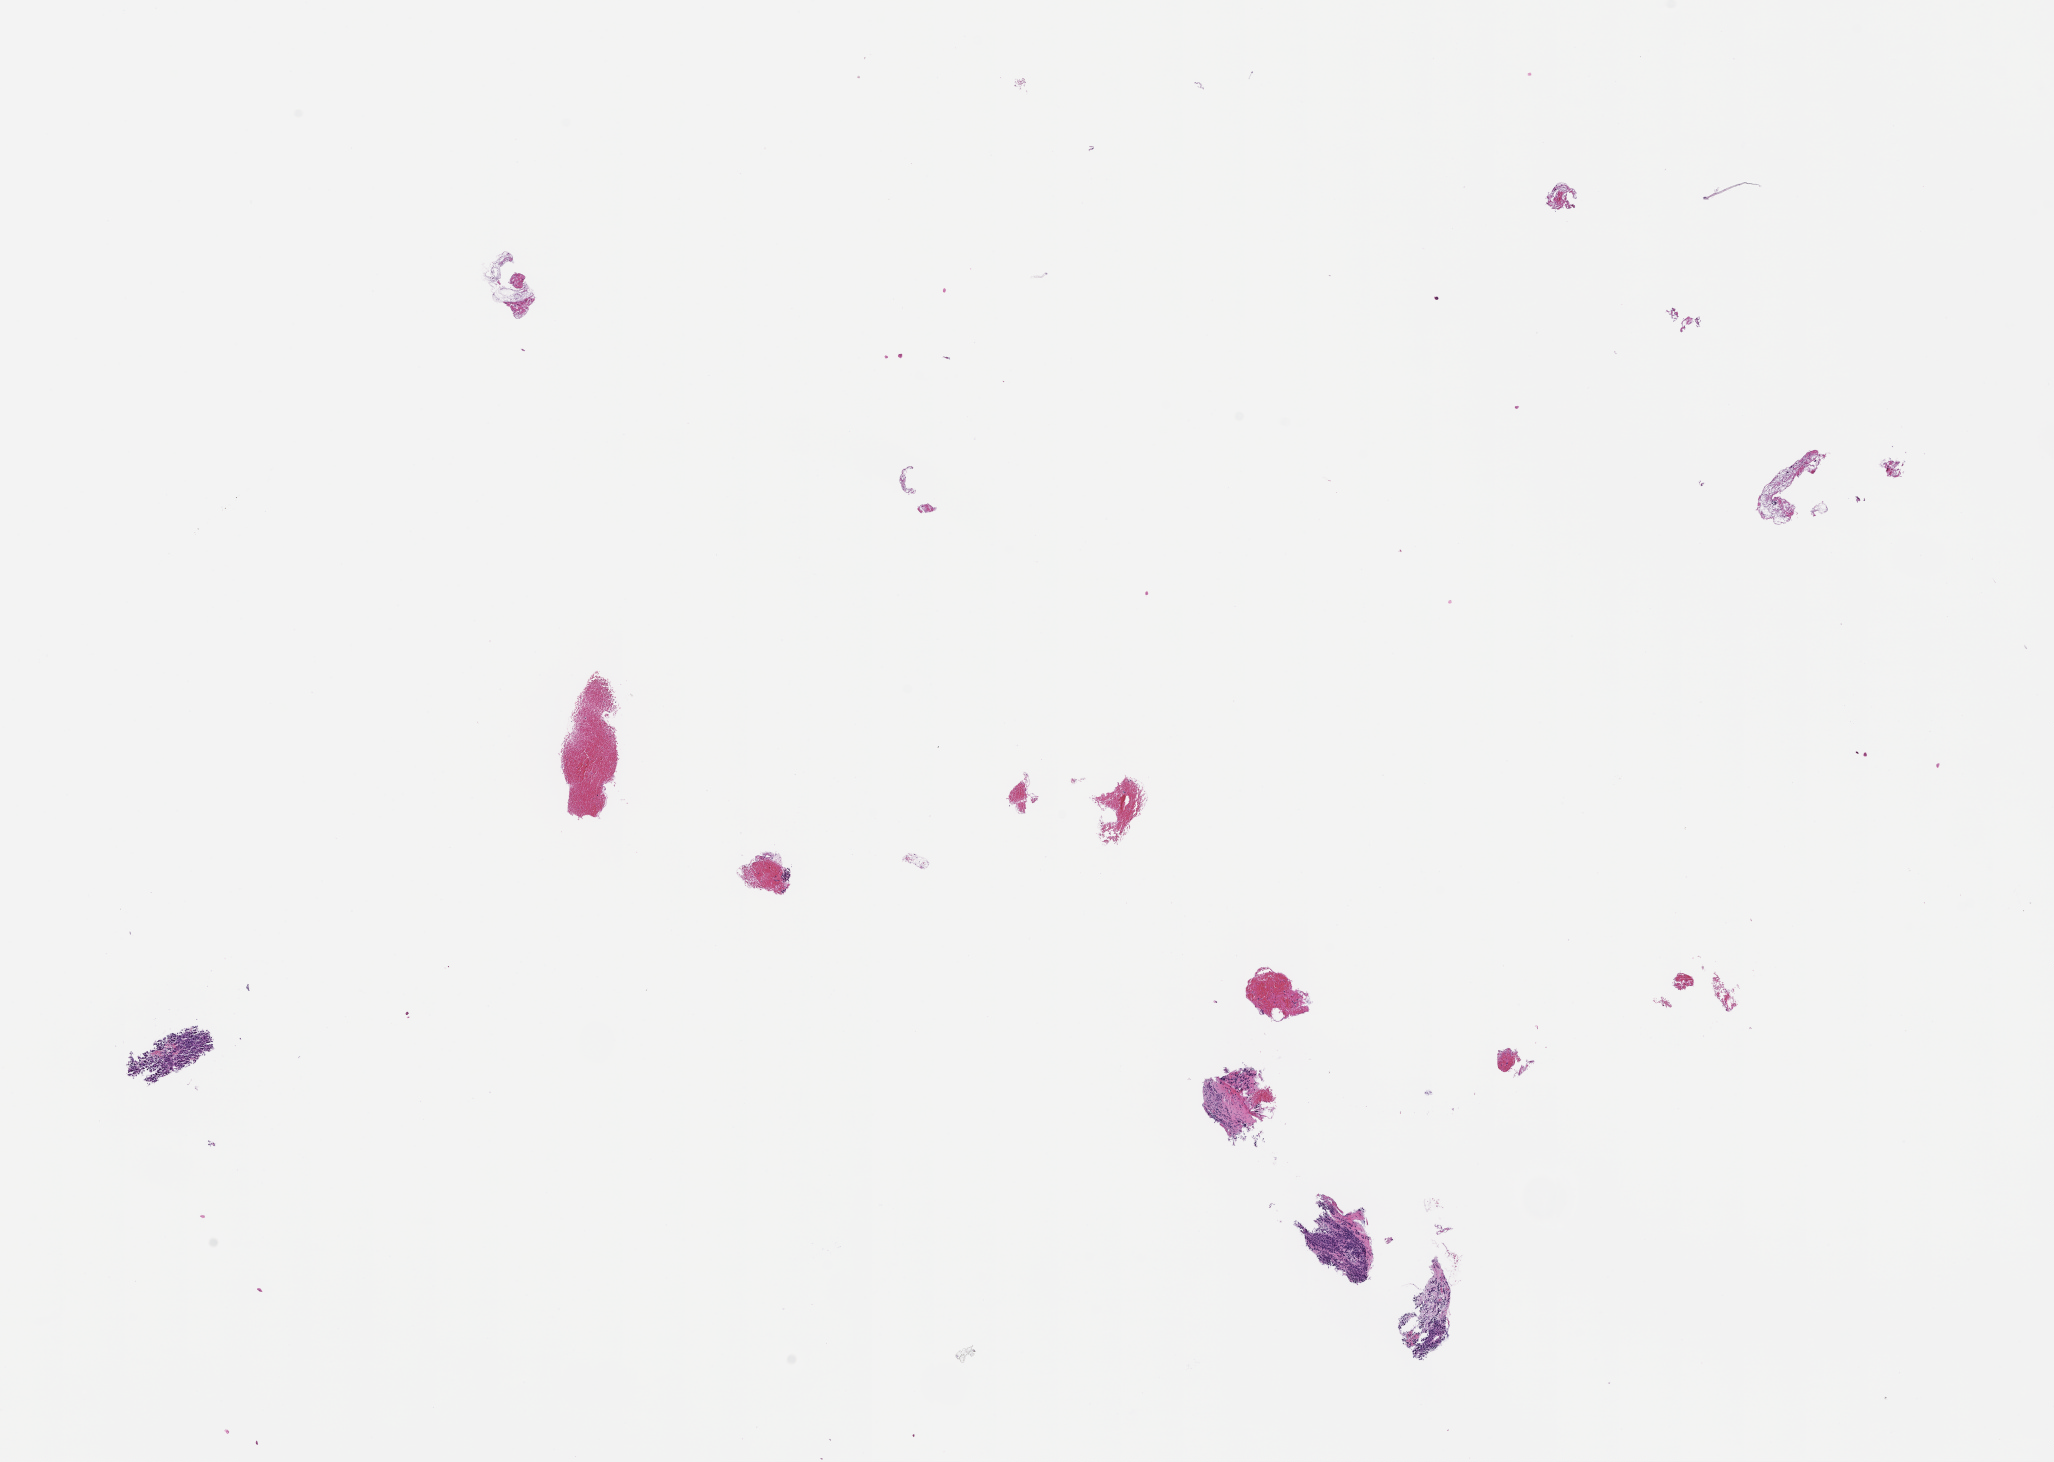
Whole-slide image, H&E stain — shown as a low-resolution overview of the whole scanned area (about 16.6 x 11.8 mm); FFPE section; collected at disease progression. Patient sex: female.
This section: metastatic tumor tissue. Primary diagnosis of the patient: Melanoma.